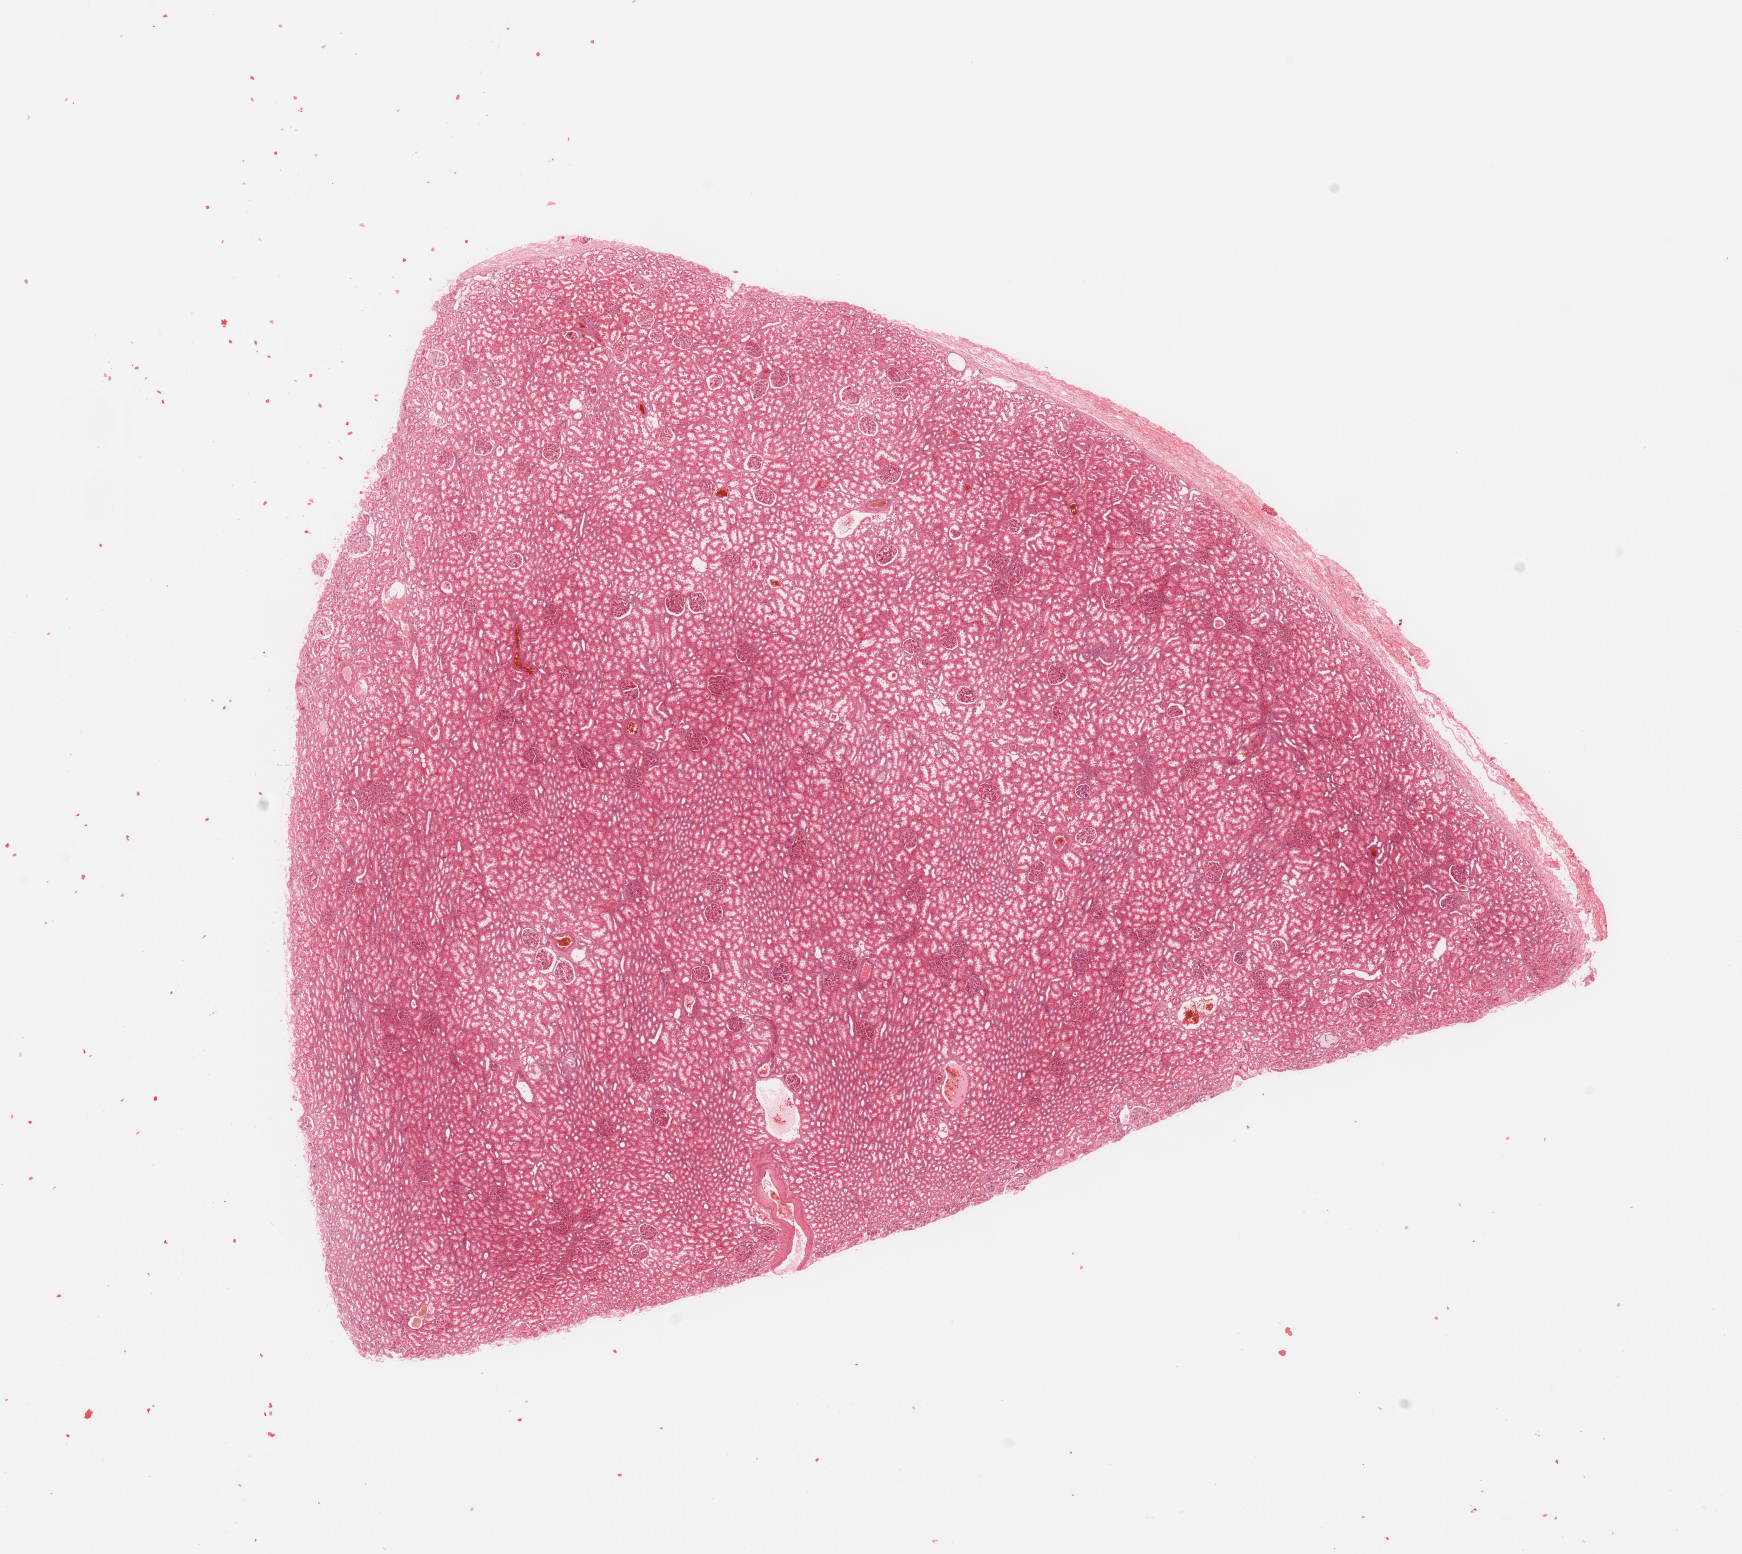
Digitized H&E tissue section (whole slide), shown as a low-resolution overview of the whole scanned area (about 13.8 x 12.3 mm, acquisition: 20x scan), kidney, normal (non-tumour) tissue. Male, 52 y/o.
- this section: normal (non-tumour) tissue from the same patient
- patient diagnosis: Renal cell carcinoma, NOS